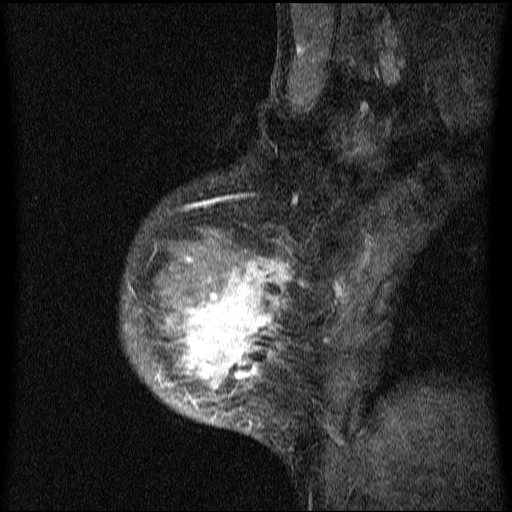
Breast MRI (dynamic contrast-enhanced), one sagittal slice; slice 52 of 64 in the series (ordered by position); dynamic contrast-enhanced series, image 2 of 4 at this slice position (ordered by acquisition); 1.5 T; TE 4.2 ms, TR 9.1 ms; 2 mm slice thickness; 512 × 512 image matrix, field of view 180 × 180 mm. Female patient, age 33 years.
Outlined on this slice (semi-automatic segmentation, software-assisted and operator-edited):
- analysis volume of interest (the breast-tissue region the enhancement analysis was run in; not a lesion): bounding box <124,151,336,447> (left, top, right, bottom; pixels)
- tumour enhancement mask (voxels above the 70 % enhancement threshold inside the analysis volume of interest): <126,206,328,430>